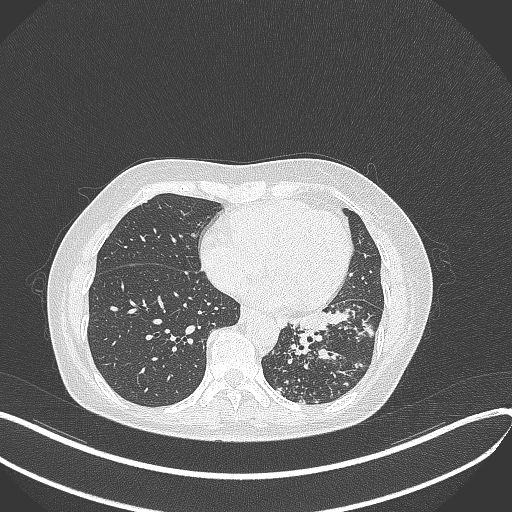
Chest CT, one axial slice; slice 147 of 429 in the series (ordered by position); reconstruction kernel B70f; lung window (W 1500 / L -600 HU); 1 mm slice thickness; 512 × 512 image matrix, field of view 400 × 400 mm. Patient: female, 63 years. From the clinical record (not read from this slice): clinical TNM (as recorded): T1b N0 M0; histopathological grade: G2-3.
Outlined on this slice (bounding box drawn by a radiologist):
- lung tumour (recorded histology: adenocarcinoma): bounding box <282,301,374,337> (left, top, right, bottom; pixels)